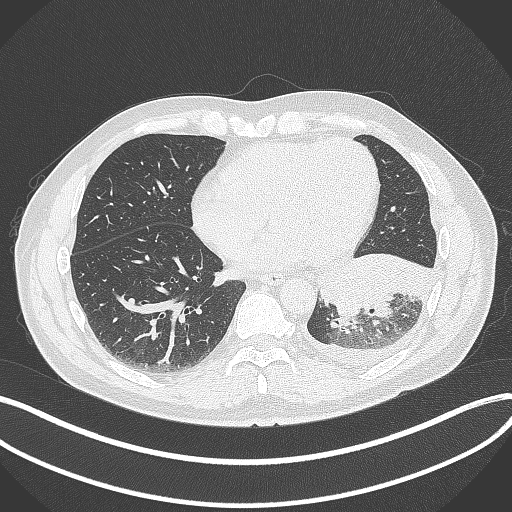
Chest CT, one axial slice; position 124 of 342 along the scan axis; lung window (W 1500 / L -600 HU); 1 mm slice thickness; 512 × 512 image matrix, field of view 400 × 400 mm. Male patient, age 58 years. Case-level facts recorded for this patient, not image findings: clinical TNM (as recorded): T3 N1 M1b; histopathological grade: G3.
Structures marked on this image (rectangle marked by the reading radiologist):
- lung tumour (recorded histology: small cell carcinoma): bounding box (x1, y1, x2, y2) in pixels: (319, 253, 437, 331)